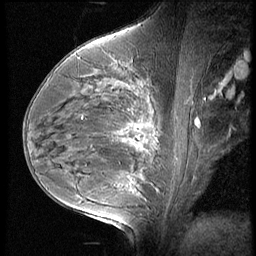
Breast MRI (dynamic contrast-enhanced), one sagittal slice; position 34 of 60 along the scan axis; 3 images stored at this slice position (order not interpretable as contrast timing); 1.5 T; TE 4.2 ms, TR 9 ms; 256 × 256 image matrix, field of view 180 × 180 mm. Female patient, age 35 years. Case-level facts recorded for this patient, not image findings: setting: breast cancer imaged before/during neoadjuvant chemotherapy; receptor status: HR-positive, HER2-negative.
Structures marked on this image (semi-automatically segmented with operator editing):
- analysis volume of interest (the breast-tissue region the enhancement analysis was run in; not a lesion): bounding box <56,58,176,202> (left, top, right, bottom; pixels)
- tumour enhancement mask (voxels above the 140 % enhancement threshold inside the analysis volume of interest): <121,127,157,189>